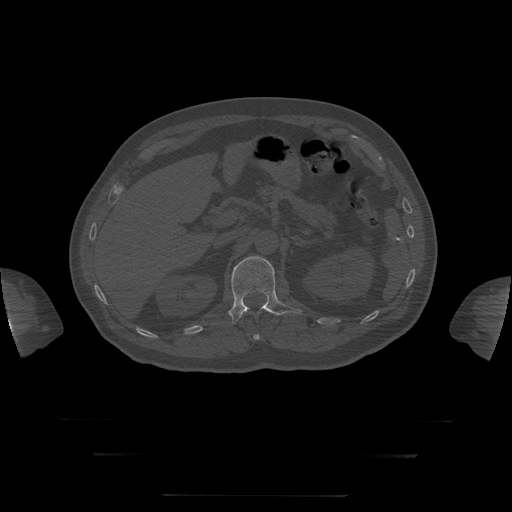
CT including the spine, one axial slice. Position 54 of 397 along the scan axis. 120 kVp. Bone window (W 1800 / L 400 HU). 512 × 512 image matrix, field of view 510 × 510 mm. Patient age 73 years. Case-level facts recorded for this patient, not image findings: primary cancer: prostate.
Structures marked on this image (semi-automatic segmentation, software-assisted and operator-edited):
- L1 vertebra: bounding box (x1, y1, x2, y2) in pixels: (229, 256, 302, 324)
- T12 vertebra: (254, 335, 260, 340)
- T8 vertebra: (237, 299, 274, 321)